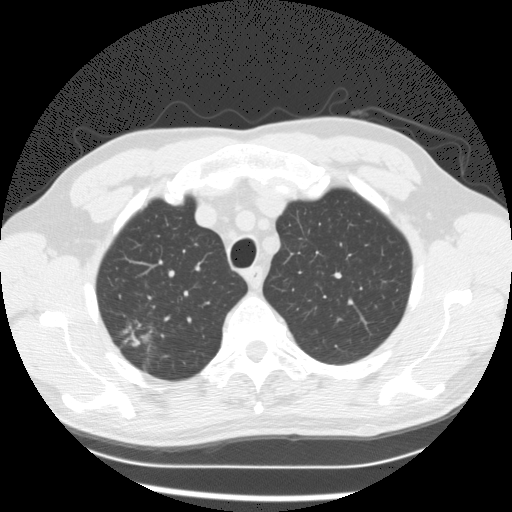
Axial slice from a low-dose chest CT screening exam, baseline screening round, lung window (W 1500 / L -600 HU), 2.5 mm slice thickness, standard (soft-tissue) reconstruction kernel (STANDARD), 120 kVp, slice 26 of 132 in the series. Male participant, aged 63 years at enrolment.
Expert reader's lesion annotation, bounding box <100,309,167,365> (left, top, right, bottom; pixels). Screening reader's record for this exam (one nodule recorded; not confirmed to be the boxed lesion): non-calcified nodule or mass ≥4 mm, right upper lobe, 19 × 9 mm, poorly defined margins, mixed attenuation. Later outcome: lung cancer diagnosed 152 days after this screen — bronchiolo-alveolar adenocarcinoma, NOS, right upper lobe, moderately differentiated (G2), stage IA (AJCC 6th edition), 15 mm at pathology.